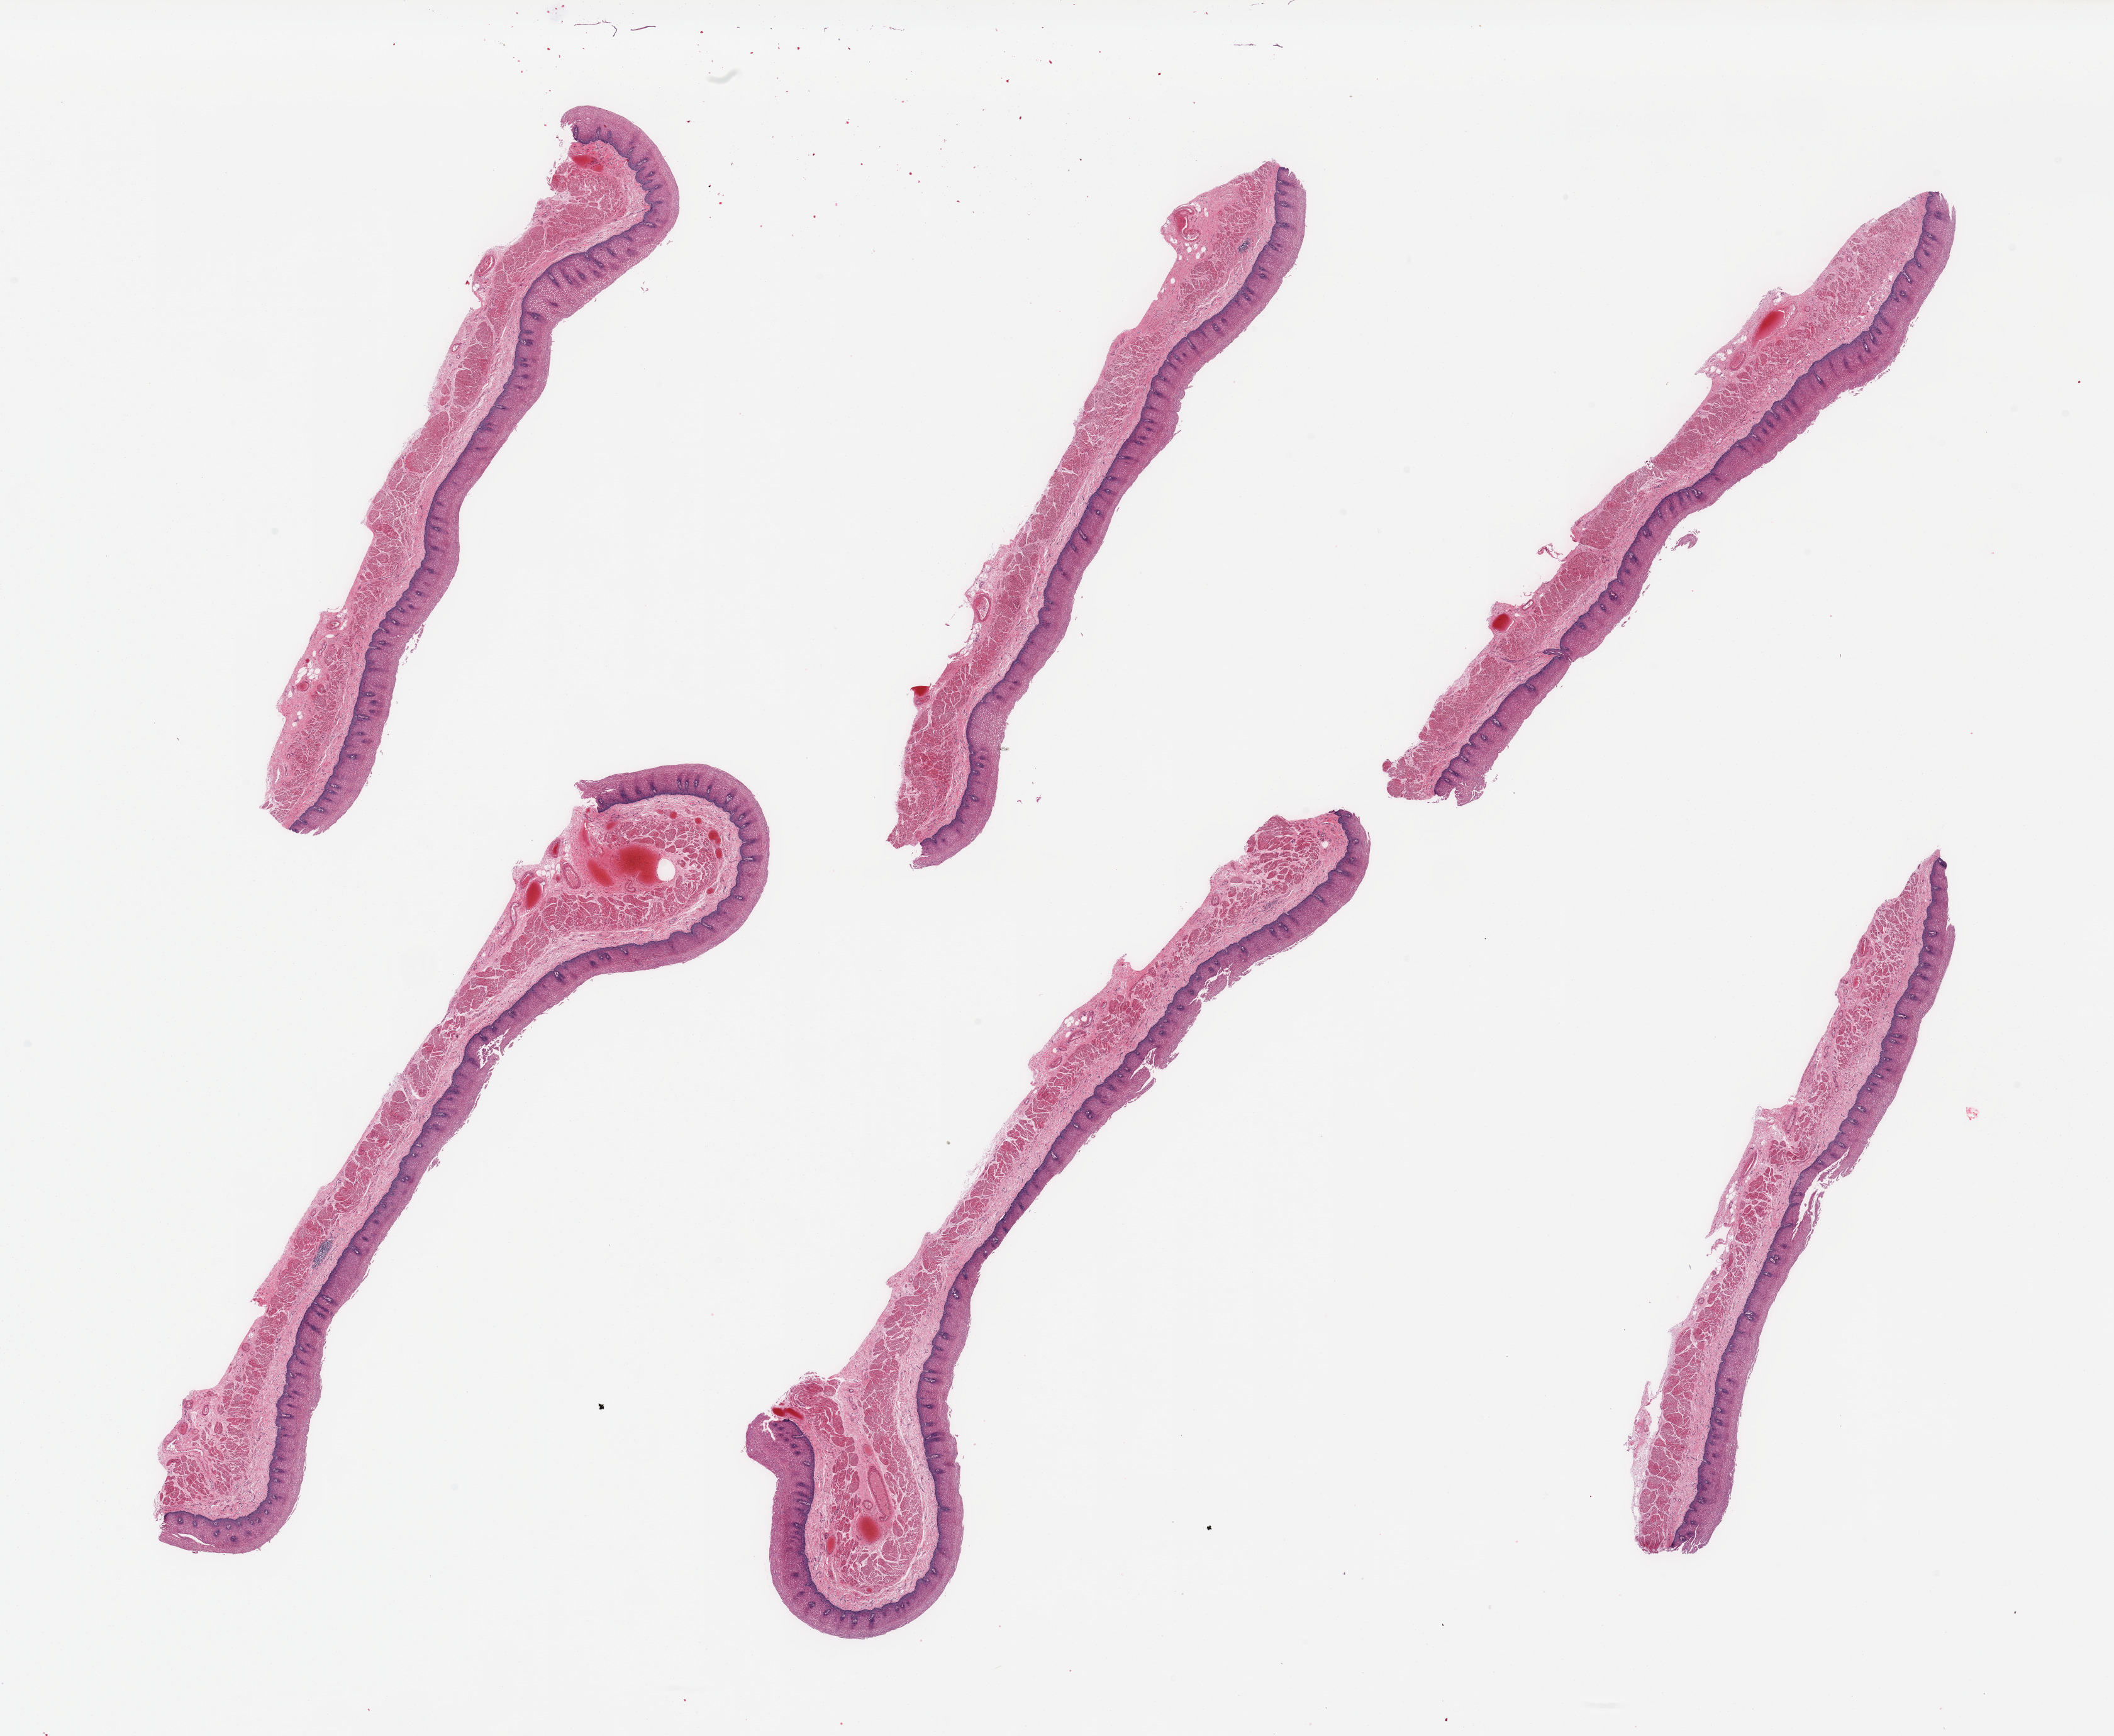
Whole-slide image, hematoxylin and eosin (H&E) stain, brightfield — a low-resolution overview of the entire scanned area, about 26.6 x 21.8 mm (slide scanned at 20x). PAXgene-fixed paraffin-embedded (PFPE) section. Section of esophageal mucous membrane (target tissue). Donor tissue sample. Donor: male.
Pathologist's review note for this sample: 6 pieces.